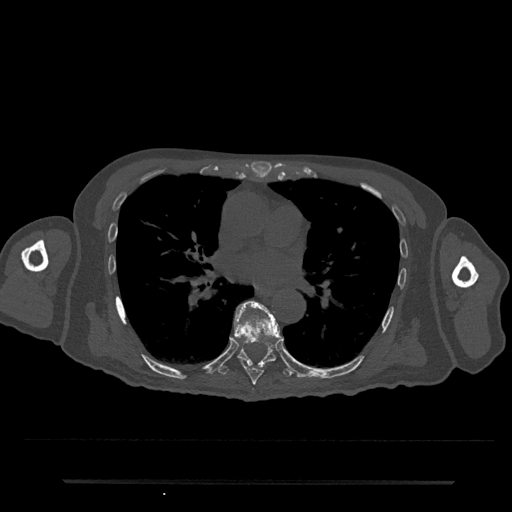
CT including the spine, one axial slice. Slice 454 of 797 in the series (ordered by position). Reconstruction kernel Br40s/3. 120 kVp. Bone window (W 1800 / L 400 HU). 0.5 mm slice thickness. 512 × 512 image matrix, field of view 427 × 427 mm. Patient: male, 74 years. Case-level facts recorded for this patient, not image findings: primary cancer: prostate.
Outlined on this slice (semi-automatic segmentation, software-assisted and operator-edited):
- T7 vertebra: bounding box [x1, y1, x2, y2] px = [234, 301, 283, 385]
- T8 vertebra: [218, 342, 293, 377]